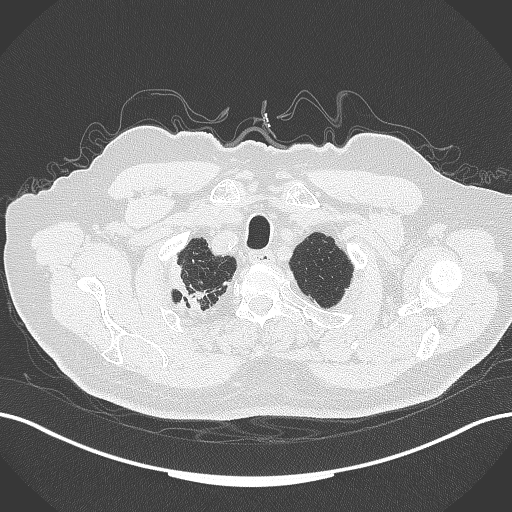
Chest CT, one axial slice; position 331 of 389 along the scan axis; 120 kVp; lung window (W 1500 / L -600 HU); 512 × 512 image matrix, field of view 400 × 400 mm. Patient: male, 72 years. Case-level facts recorded for this patient, not image findings: clinical TNM (as recorded): T1a N0 M0.
Outlined on this slice (bounding box drawn by a radiologist):
- lung tumour (recorded histology: squamous cell carcinoma): bounding box (x1, y1, x2, y2) in pixels: (161, 257, 215, 317)